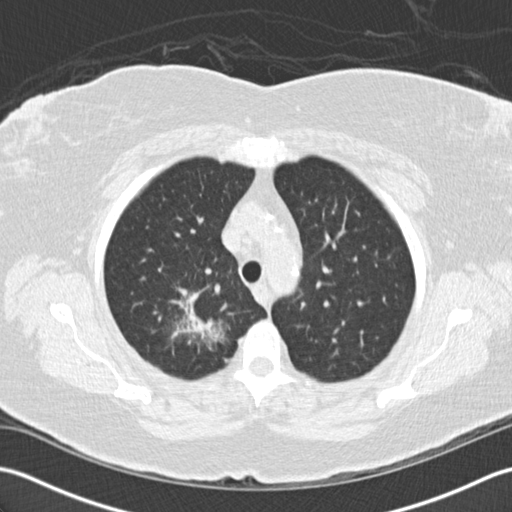
Low-dose screening chest CT, axial slice; baseline annual screen; lung window (W 1500 / L -600 HU); 2 mm slice thickness; standard (soft-tissue) reconstruction kernel (B30f). Female, age 72 years at enrolment.
Expert-annotated lung lesion, bounding box [x1, y1, x2, y2] px = [138, 274, 235, 368]. The screening reader recorded 2 non-calcified nodules or masses ≥4 mm on this exam (right lower lobe, right lower lobe); which of them this box marks is not recorded. Lung cancer was diagnosed 494 days after this screen: bronchiolo-alveolar adenocarcinoma, NOS, right upper lobe, stage IIIB (AJCC 6th edition), 45 mm at pathology.